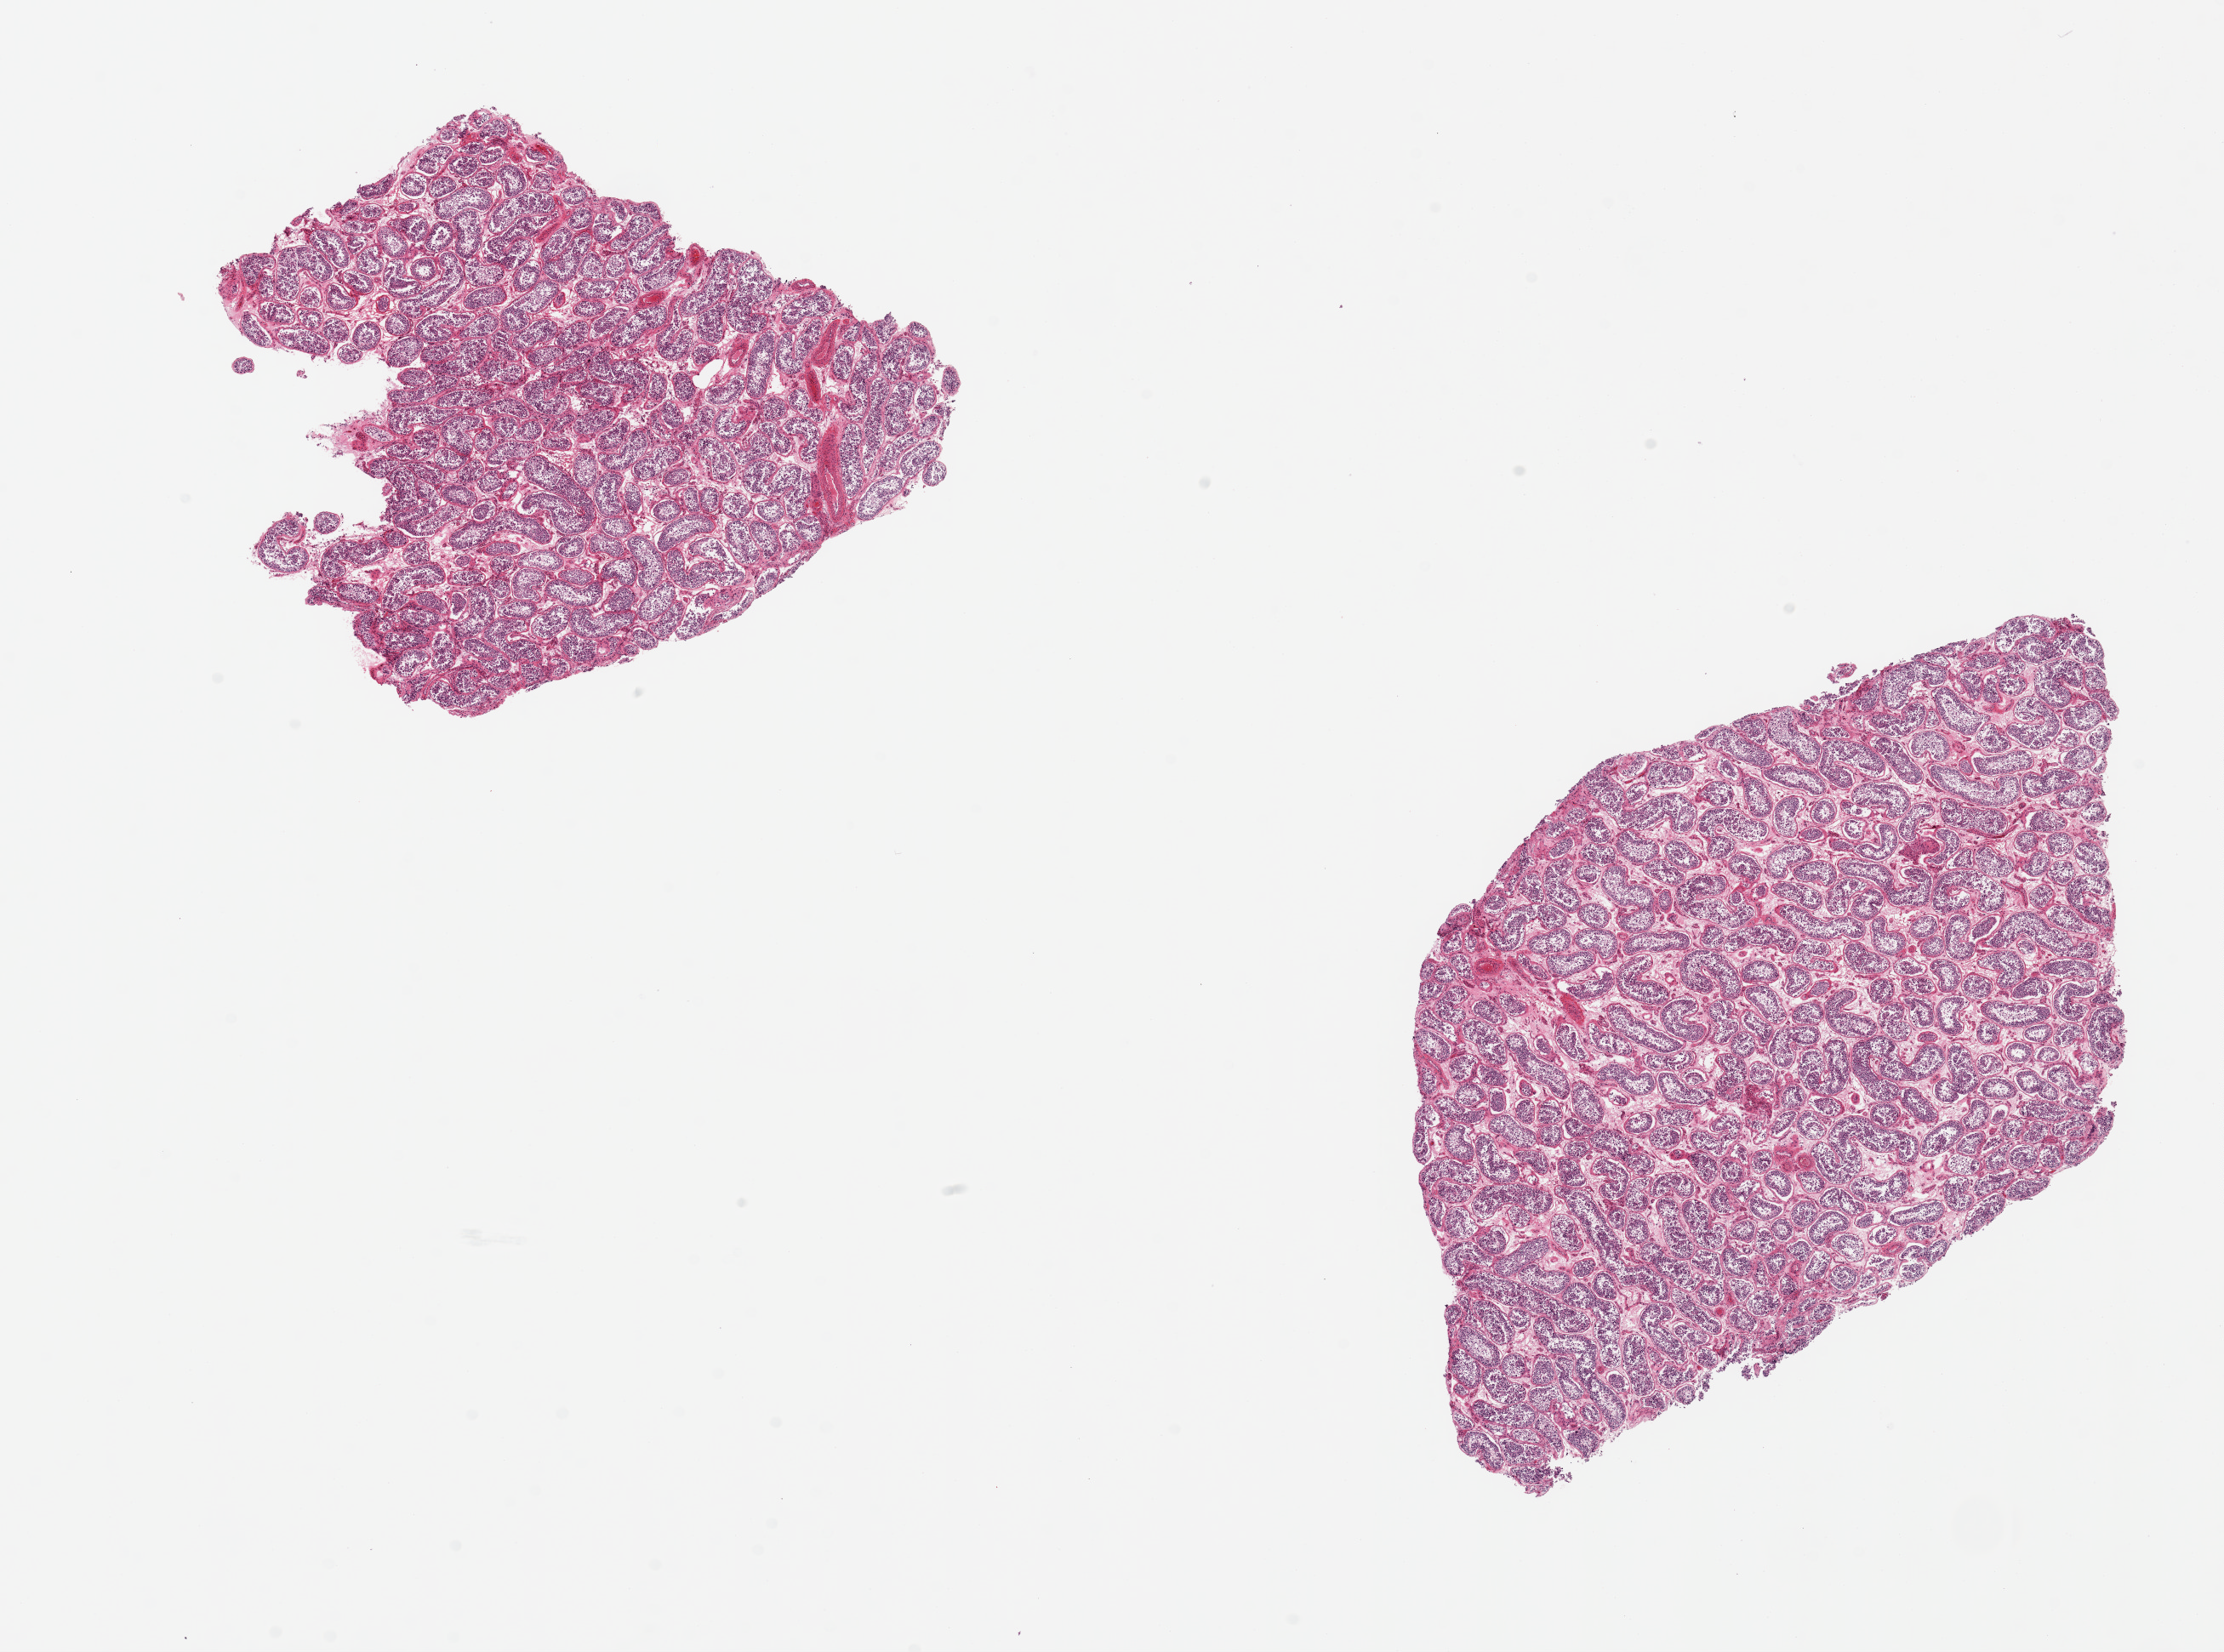
Whole-slide image, hematoxylin and eosin (H&E) stain, brightfield — a low-resolution overview of the entire scanned area, about 20.7 x 15.4 mm (acquisition: 20x scan); PAXgene-fixed paraffin-embedded (PFPE) section; section of testis (target tissue); donor tissue sample. Male donor.
Reviewer comment on this tissue sample: 2 pieces, 6x5.5 & 7x6mm; spermatogenesis.